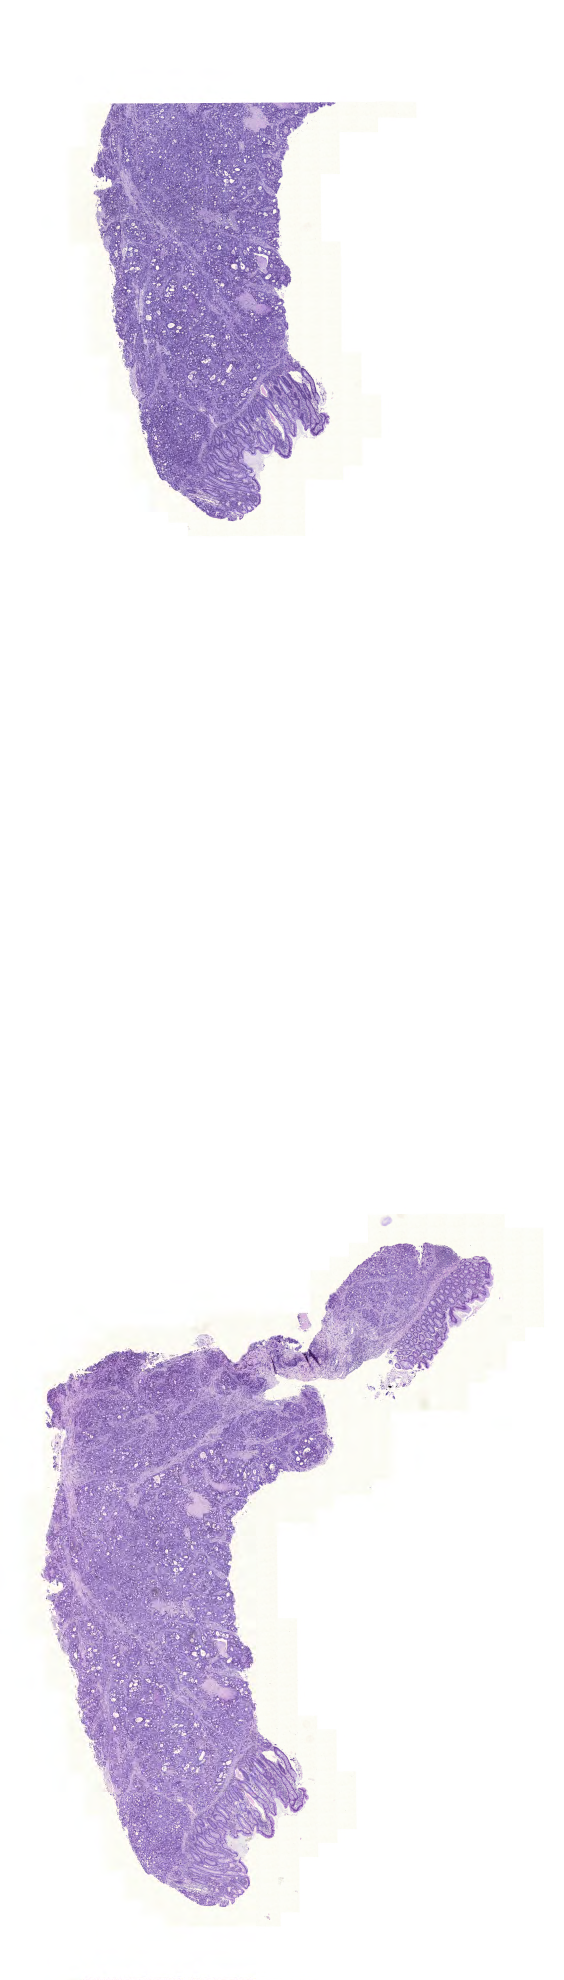
H&E-stained whole-slide image, low-resolution overview of the scanned area, about 8.4 x 29.5 mm (acquisition: 20x scan), formalin-fixed paraffin-embedded (FFPE) diagnostic section, sample: primary tumour, colon. Female, age 84 years at initial diagnosis.
- TNM: T3 N2 M0
- pathologic diagnosis: Adenocarcinoma with neuroendocrine differentiation
- AJCC pathologic stage: III
- lymph nodes positive (case pathology): 5 of 15 examined